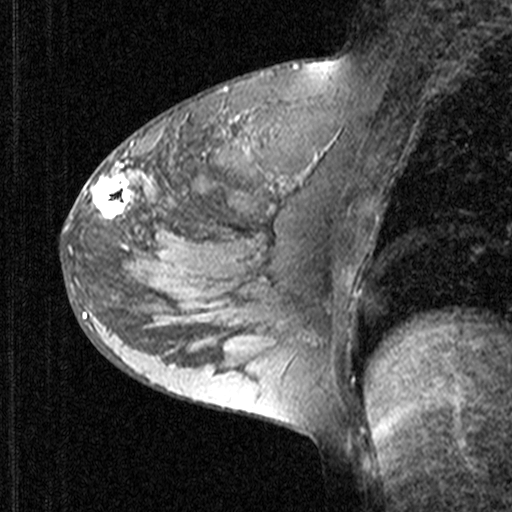
Breast MRI (dynamic contrast-enhanced), one sagittal slice; slice 22 of 44 in the series (ordered by position); dynamic contrast-enhanced study with each time point stored as its own series, time point 2 of 3 at this slice position (early post-contrast, ordered by acquisition time); 1.5 T; TE 4.5 ms, TR 11 ms; 3 mm slice thickness; 512 × 512 image matrix. Female patient, age 27 years. From the clinical record (not read from this slice): setting: breast cancer imaged before/during neoadjuvant chemotherapy; receptor status: HR-positive, HER2-negative.
Annotated regions visible in this slice (semi-automatically segmented with operator editing):
- analysis volume of interest (the breast-tissue region the enhancement analysis was run in; not a lesion): bounding box <68,146,165,239> (left, top, right, bottom; pixels)
- tumour enhancement mask (voxels above the 90 % enhancement threshold inside the analysis volume of interest): <71,175,132,220>